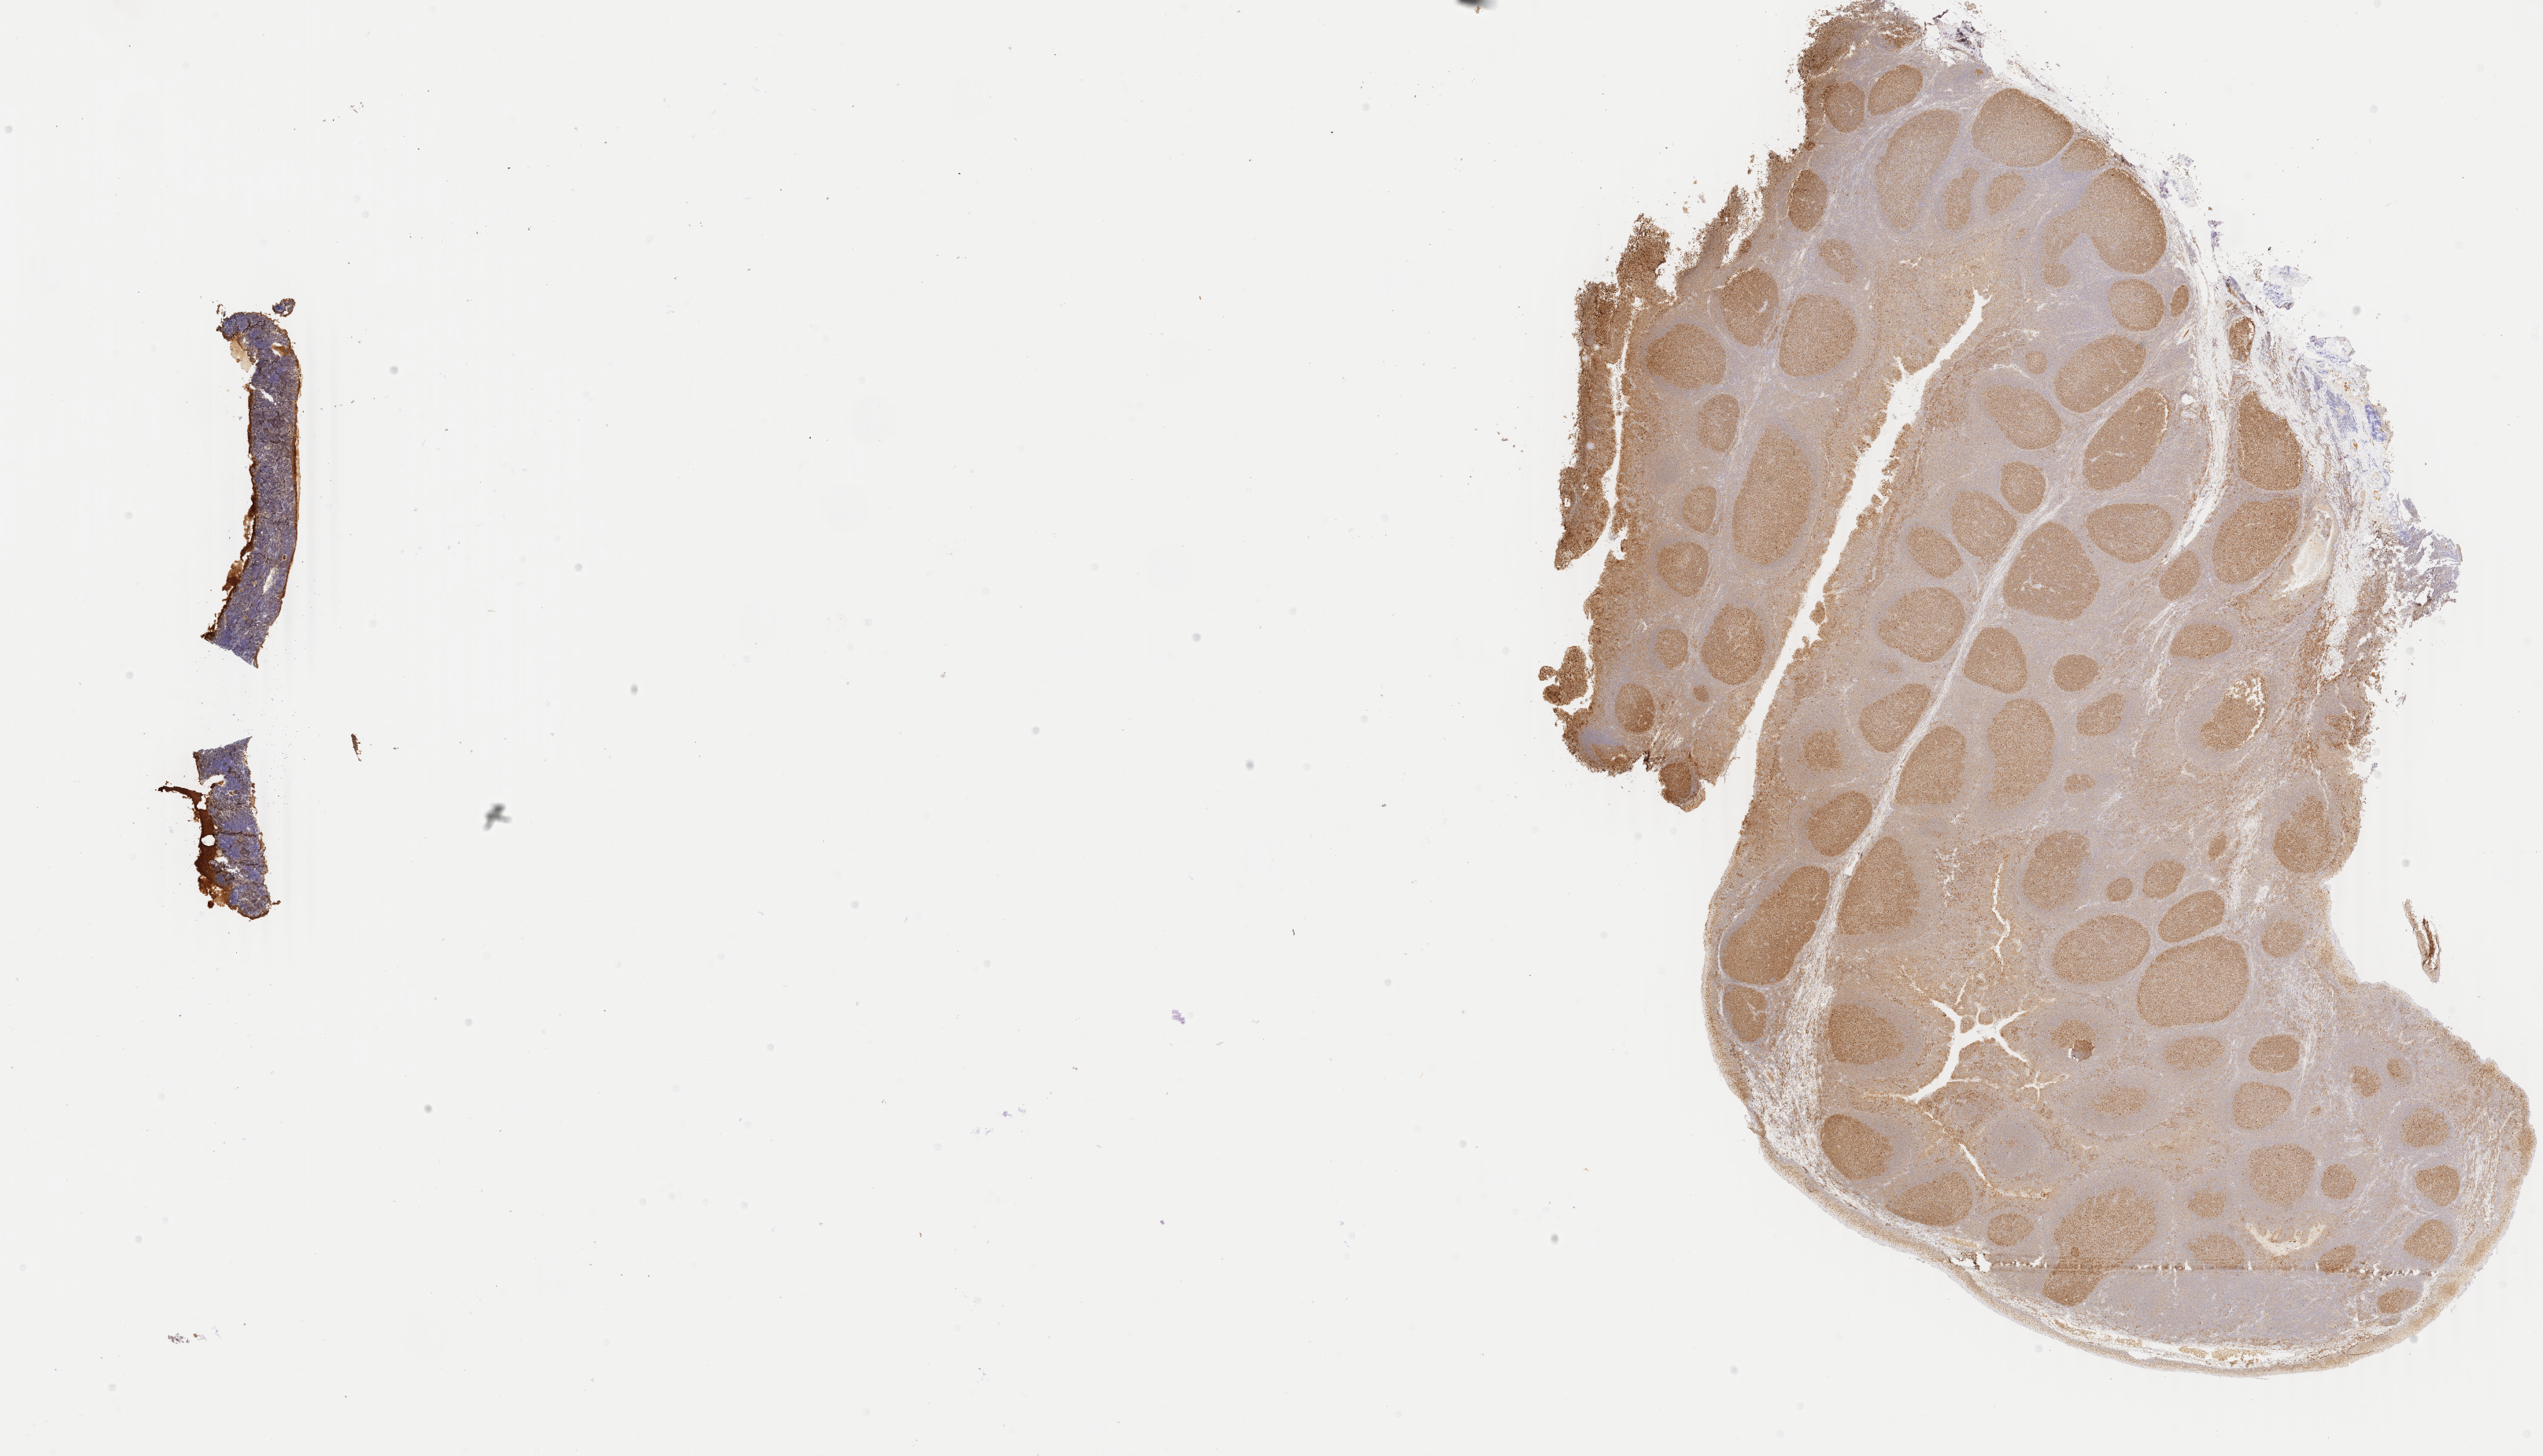
IHC for BCL6, whole-slide image — whole scanned area (about 25.7 x 14.7 mm) shown as a low-resolution overview; tumor tissue; site: abdominal lymph node. Female patient; age at initial diagnosis 6 years.
Diagnosis: Burkitt lymphoma, NOS.